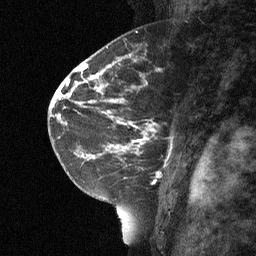
Breast MRI (dynamic contrast-enhanced), one sagittal slice. Dynamic contrast-enhanced study with each time point stored as its own series, time point 2 of 3 at this slice position (early post-contrast, ordered by acquisition time). 1.5 T. TE 4.8 ms, TR 27 ms. 2 mm slice thickness. 256 × 256 image matrix, field of view 180 × 180 mm. Female patient, age 42 years. From the clinical record (not read from this slice): setting: breast cancer imaged before/during neoadjuvant chemotherapy; receptor status: triple-negative.
Structures marked on this image (semi-automatic segmentation, software-assisted and operator-edited):
- analysis volume of interest (the breast-tissue region the enhancement analysis was run in; not a lesion): bounding box <115,86,182,160> (left, top, right, bottom; pixels)
- tumour enhancement mask (voxels above the 90 % enhancement threshold inside the analysis volume of interest): <115,99,144,151>